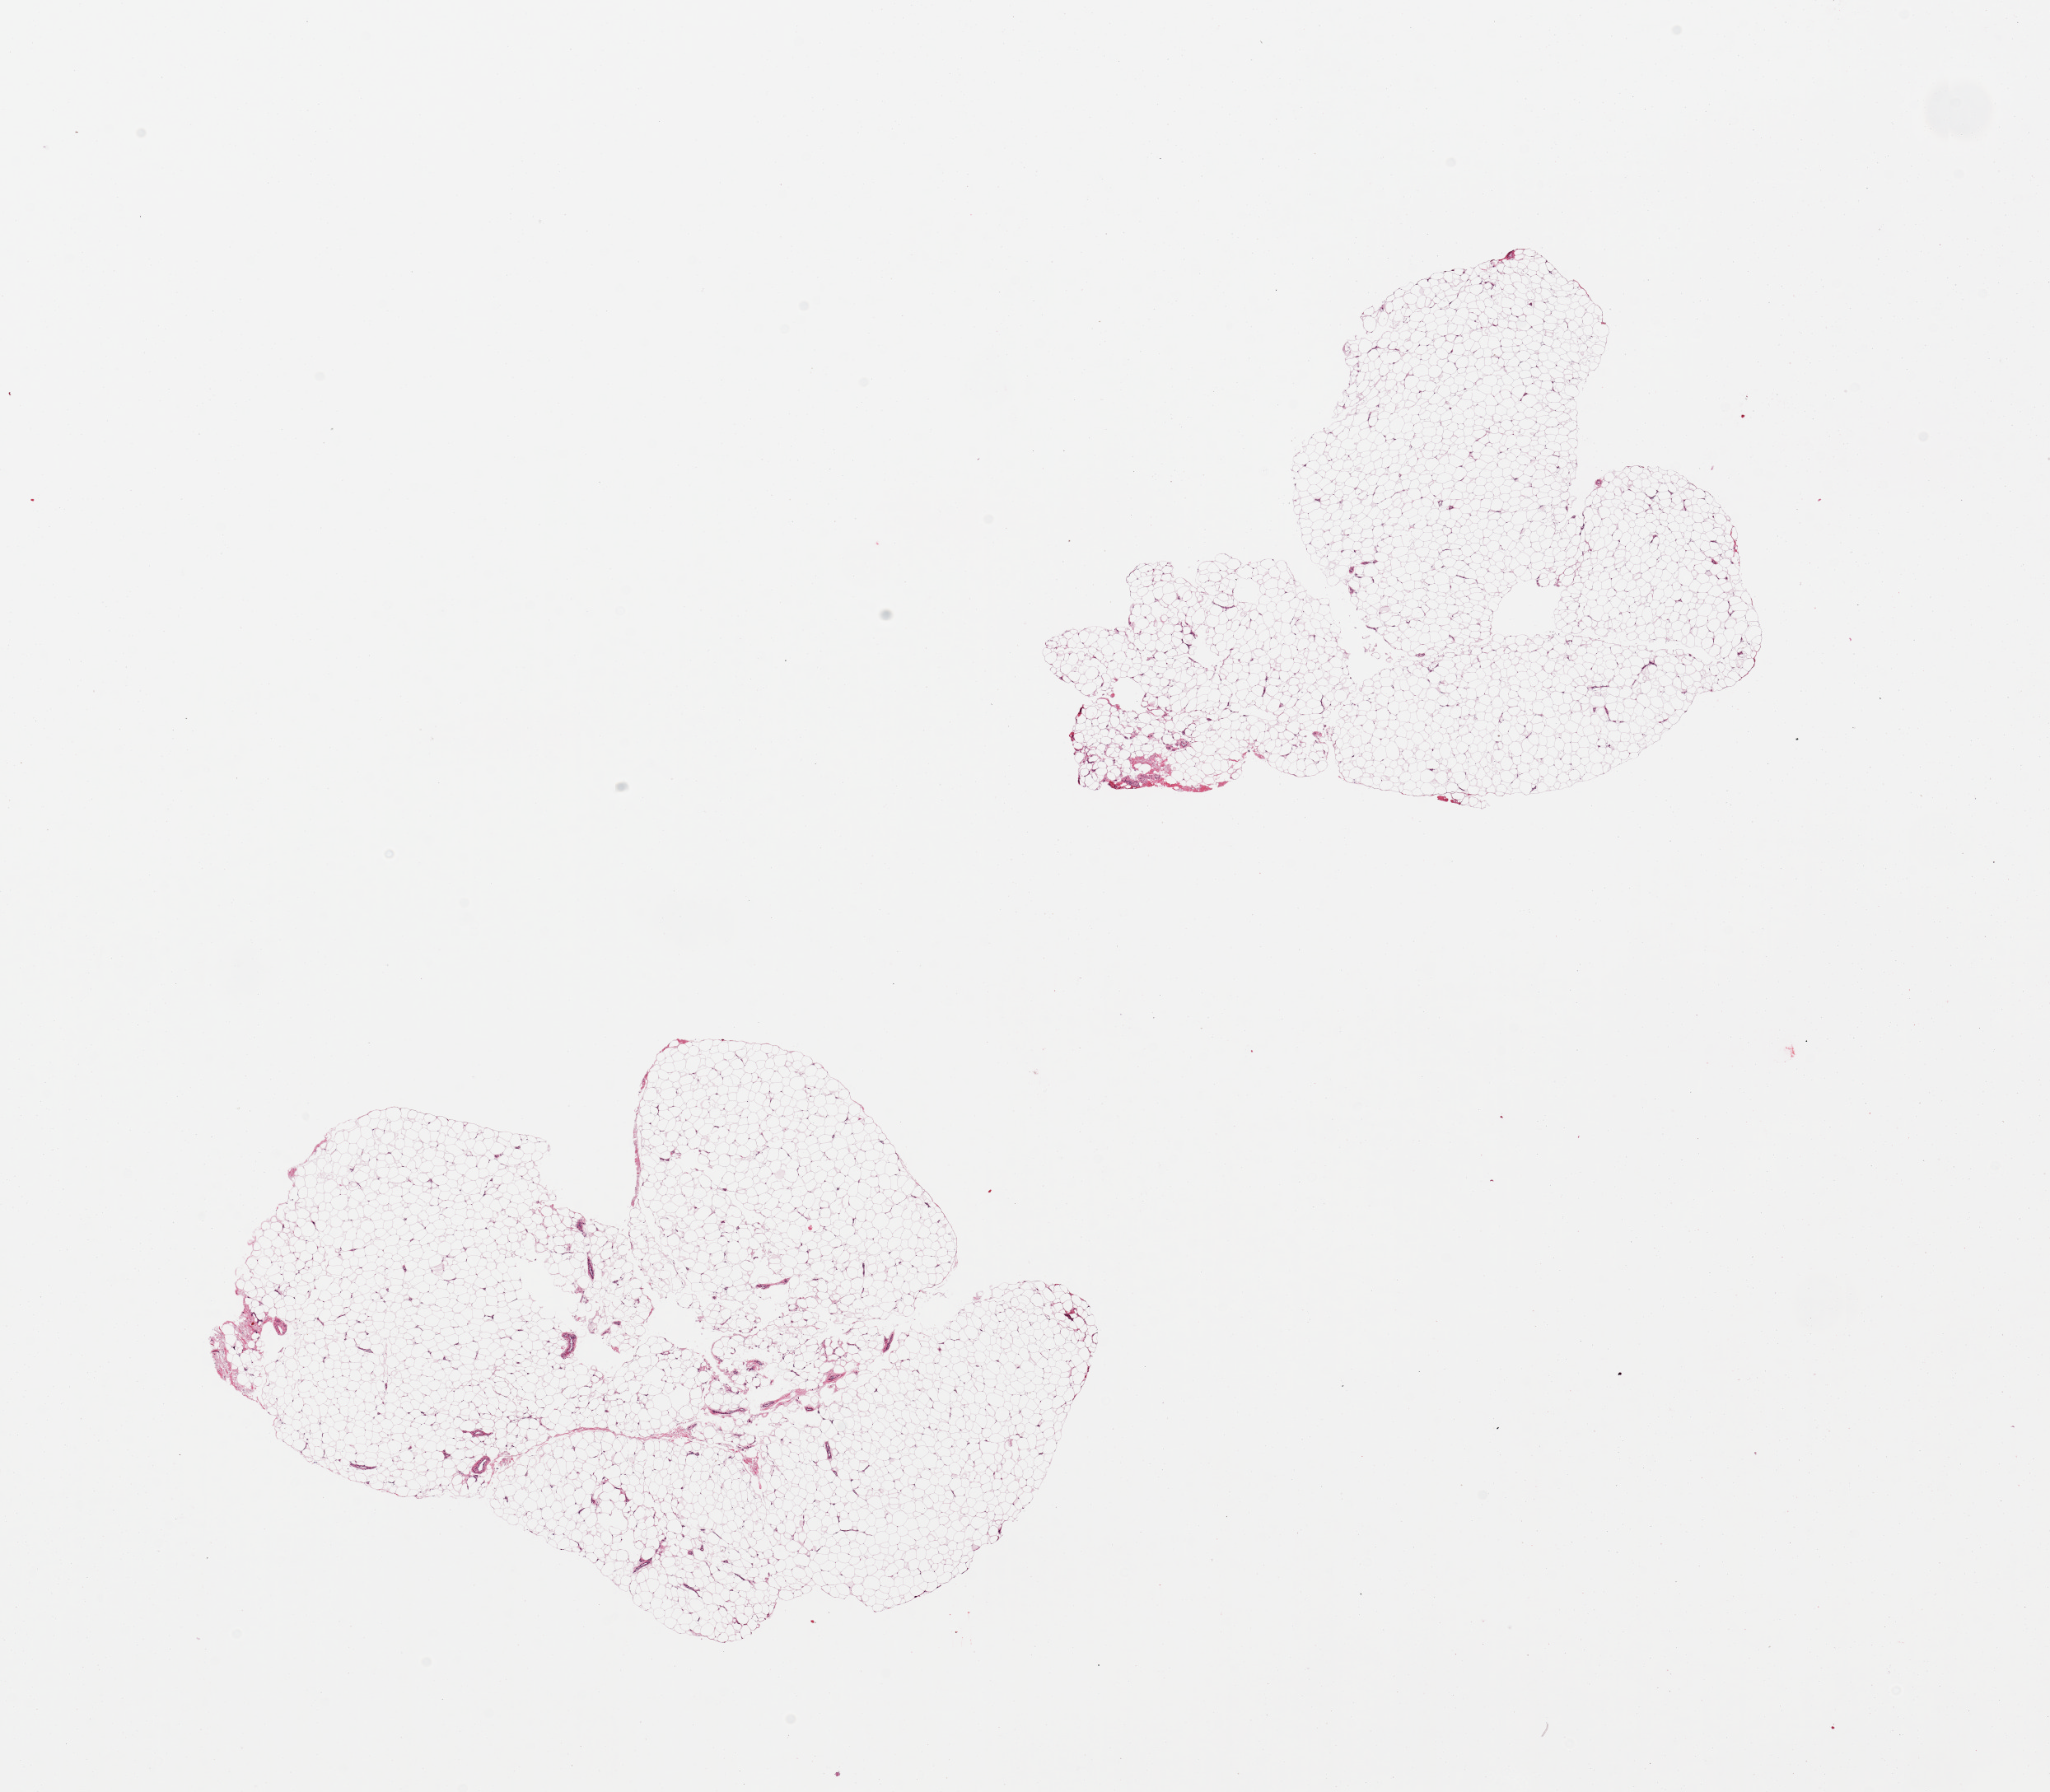
Digitized H&E-stained section — low-resolution overview of the scanned area, about 19.7 x 17.2 mm, PAXgene-fixed paraffin-embedded (PFPE) section, section of adipose tissue (target tissue), tissue donor sample.
- reviewer comment on this tissue sample: 2 pieces, no fascia/vascular tissue